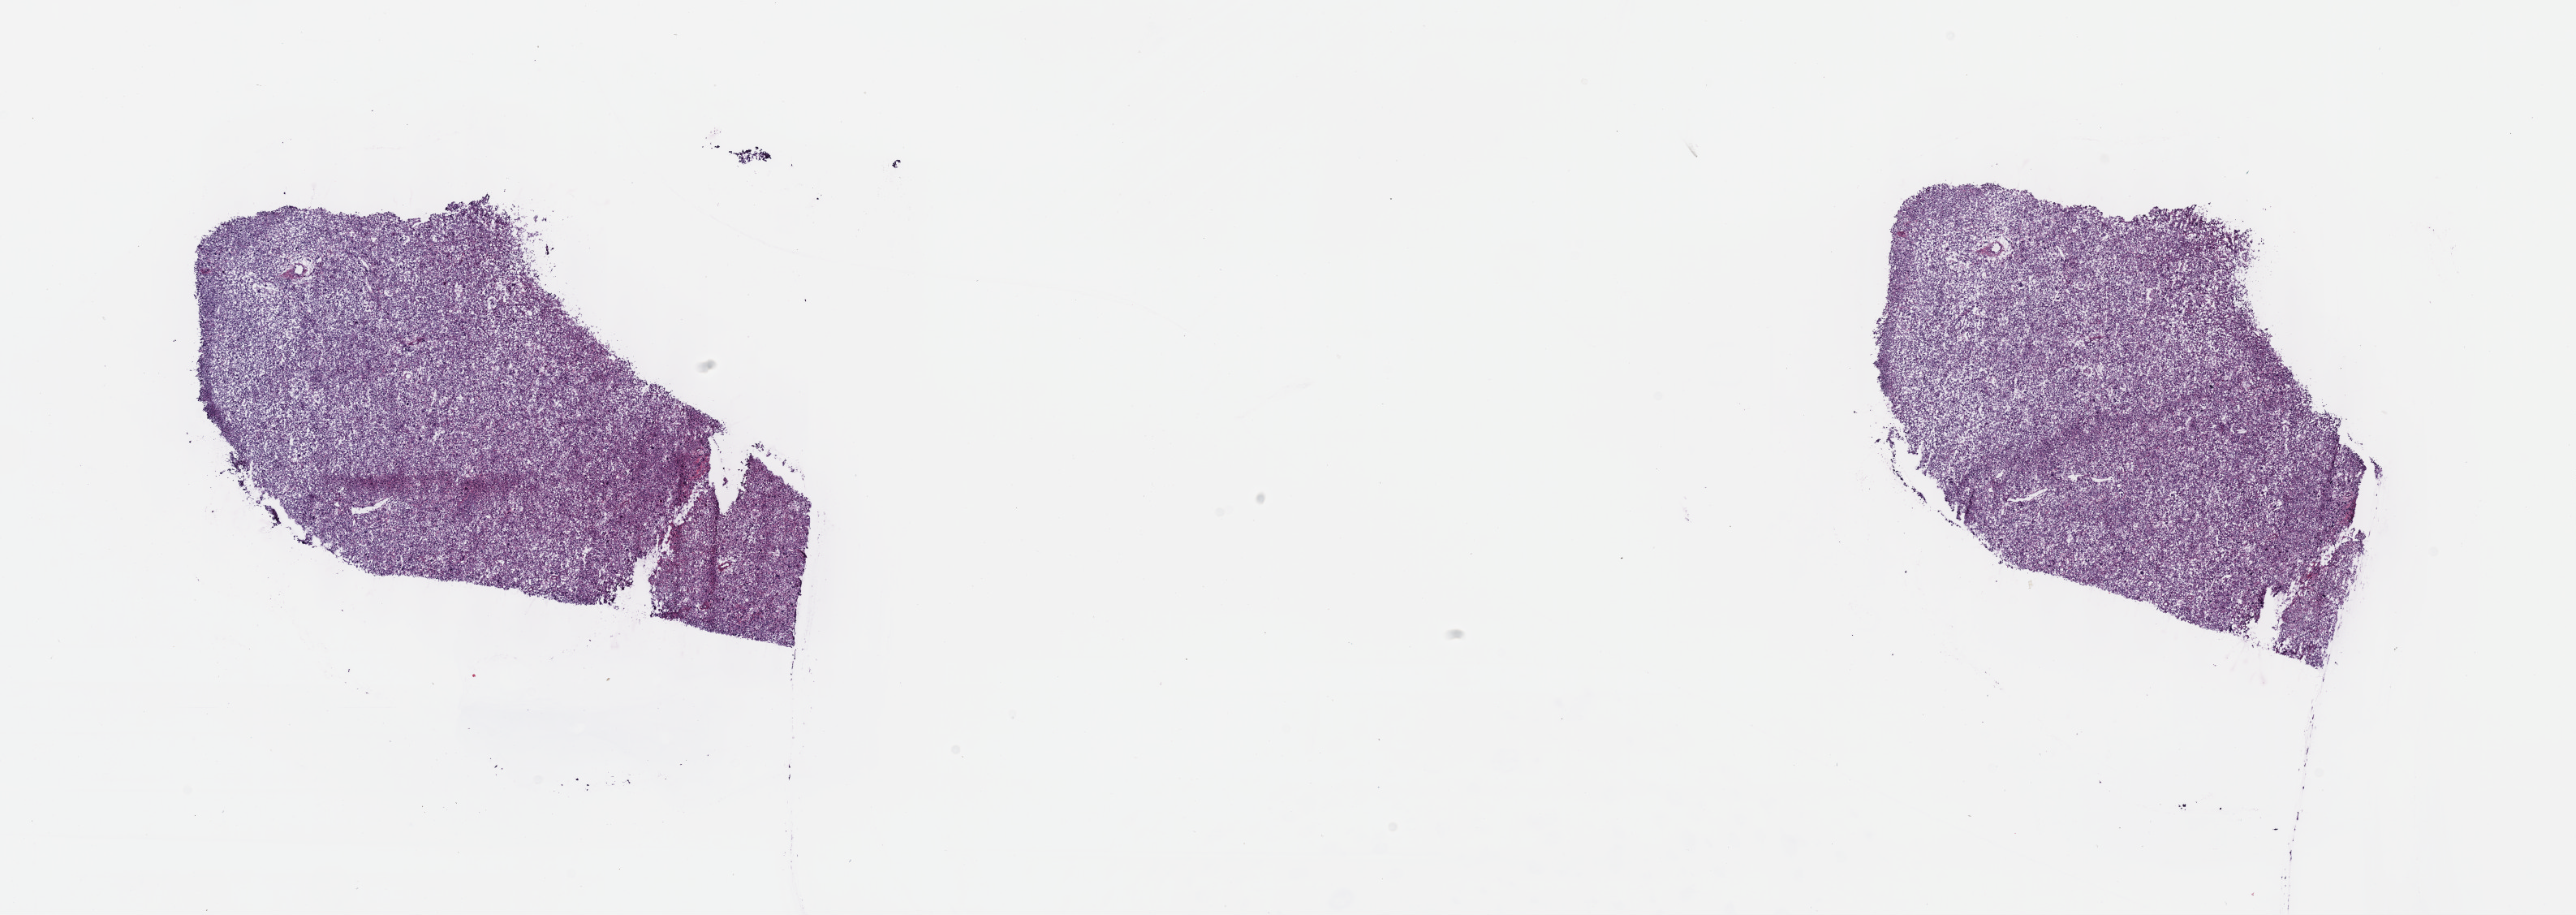
Digitized H&E-stained tissue section (whole slide) — shown as a low-resolution overview of the whole scanned area (about 25.7 x 9.1 mm, acquisition: 40x scan), frozen section, connective, subcutaneous and other soft tissues, primary tumour sample. Female patient; age at initial diagnosis 61 years. Pathologist review of this section (percent, as recorded): tumour cells 100%, tumour nuclei 80%, normal cells 0%, stromal cells 0%, necrosis 0%. Inflammatory infiltration, as recorded: lymphocyte infiltration 2%, monocyte infiltration 0%, neutrophil infiltration 0%.
Pathologic diagnosis: Undifferentiated sarcoma (connective, subcutaneous and other soft tissues of lower limb and hip).